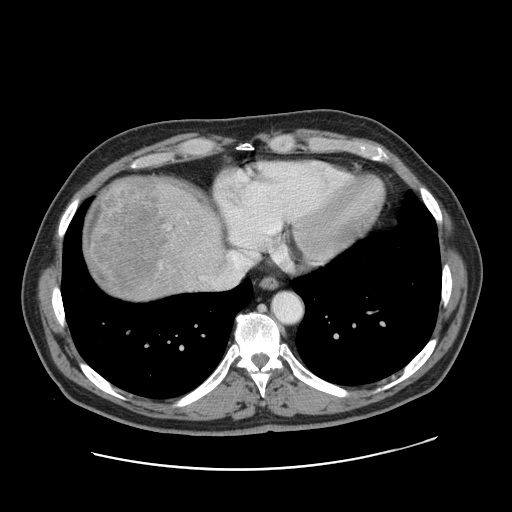
Contrast-enhanced abdominal CT, one axial slice. Slice 148 of 178 in the series (ordered by position). Intravenous contrast given. Soft-tissue window (W 400 / L 40 HU). 2.5 mm slice thickness. 512 × 512 image matrix, field of view 403 × 403 mm. Male patient, age 63 years. Case-level facts recorded for this patient, not image findings: diagnosis: colorectal cancer liver metastases, imaged before liver resection; multiple liver metastases: yes; largest metastasis: 8 cm; disease in both lobes: yes.
Outlined on this slice (outlined manually by an expert reader):
- hepatic veins: bounding box [x1, y1, x2, y2] px = [212, 252, 252, 287]
- liver: [82, 177, 225, 301]
- planned liver remnant (the part of the liver to remain after resection): [185, 192, 225, 258]
- liver metastasis: [85, 181, 165, 298]